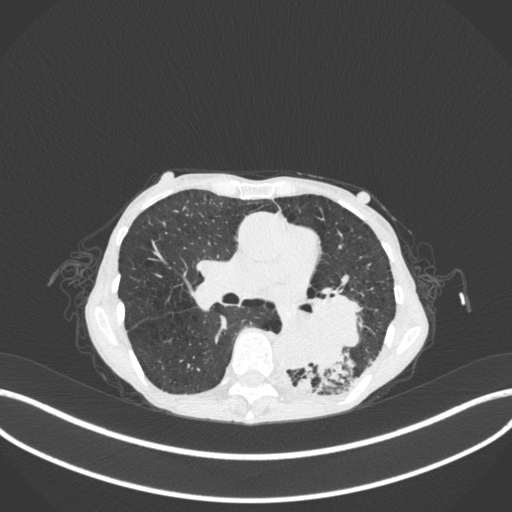
Chest CT, one axial slice. Slice 145 of 347 in the series (ordered by position). 120 kVp. Lung window (W 1500 / L -600 HU). 1 mm slice thickness. 512 × 512 image matrix, field of view 400 × 400 mm. Female patient, age 70 years. Case-level facts recorded for this patient, not image findings: clinical TNM (as recorded): T3 N0 M0; histopathological grade: G3.
Structures marked on this image (rectangle marked by the reading radiologist):
- lung tumour (recorded histology: small cell carcinoma): bounding box <288,282,367,374> (left, top, right, bottom; pixels)